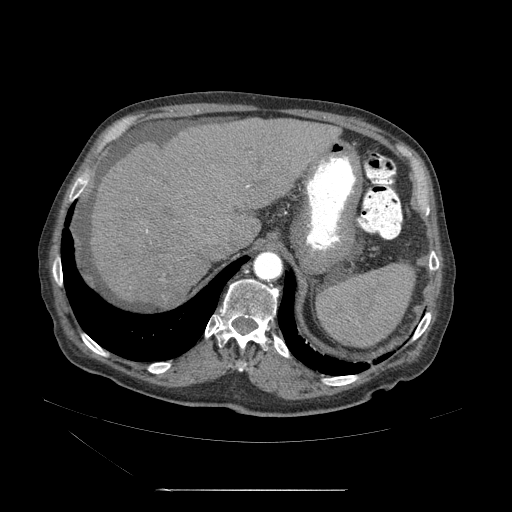
Contrast-enhanced abdominal CT (liver protocol), one axial slice. Slice 39 of 71 in the series (ordered by position). Reconstruction kernel STANDARD. 120 kVp. Soft-tissue window (W 400 / L 40 HU). 2.5 mm slice thickness. 512 × 512 image matrix, field of view 440 × 440 mm. From the clinical record (not read from this slice): diagnosis: hepatocellular carcinoma (patient treated with transarterial chemoembolisation; whether this scan precedes or follows treatment is not stated here); TNM stage (as recorded): Stage-II; Child-Pugh class: A; tumour size: 1 cm.
Annotated regions visible in this slice (semi-automatically segmented with operator editing):
- abdominal aorta: bounding box [x1, y1, x2, y2] px = [254, 253, 284, 282]
- liver parenchyma outside the tumour (the mass and vessels are separate outlines, so this box may not span the whole liver): [80, 119, 340, 314]
- mass: [152, 283, 184, 312]
- liver vessels: [127, 164, 233, 264]